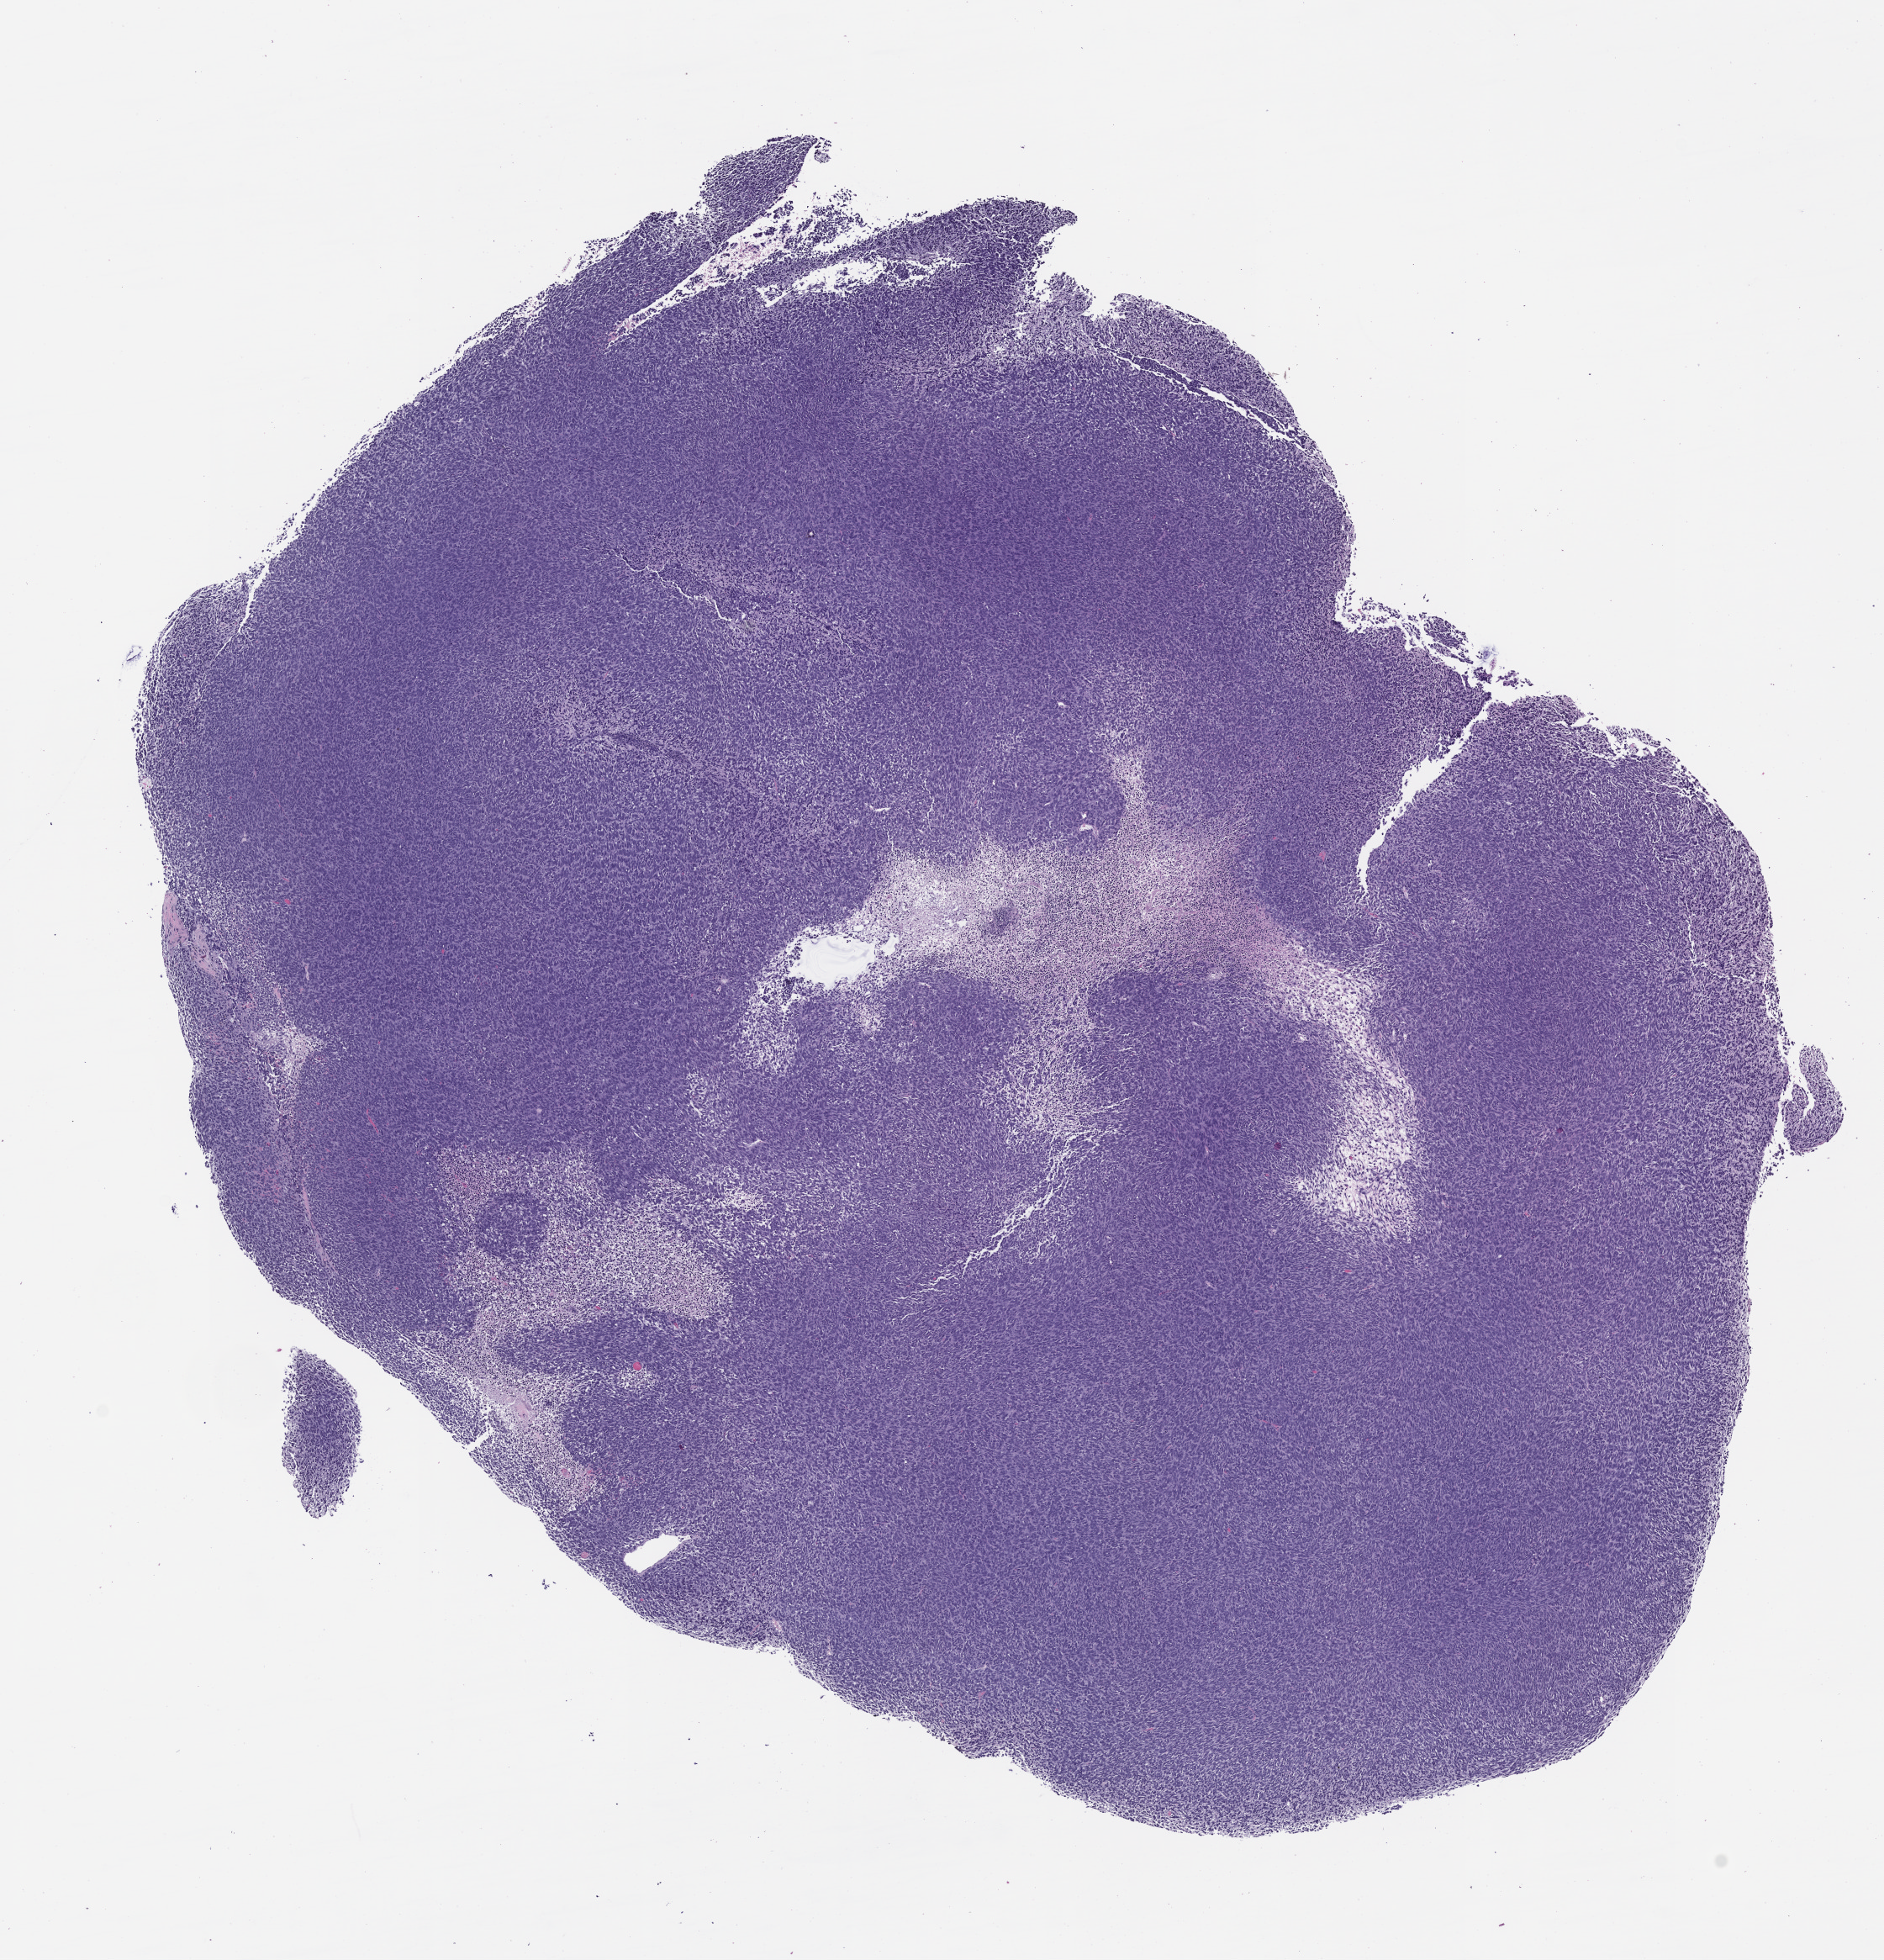
Whole-slide image, H&E: patient-derived xenograft (human tumor grown in a mouse), passage 0, low-resolution overview of the scanned area, about 9.0 x 9.4 mm, formalin-fixed, paraffin-embedded (FFPE) tissue, originating tumor site category: musculoskeletal.
Originating patient diagnosis: Synovial Sarcoma.